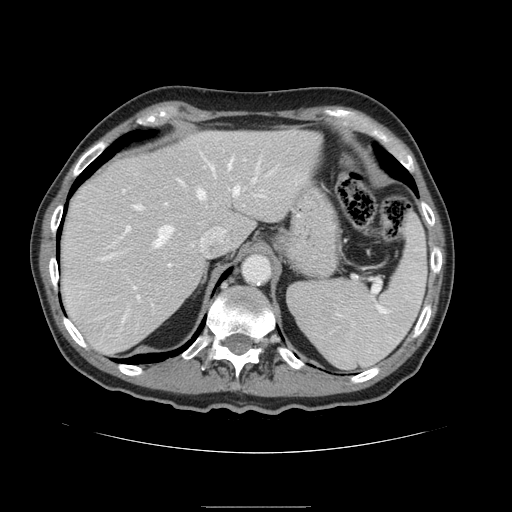
Contrast-enhanced abdominal CT, one axial slice. Position 115 of 168 along the scan axis. 120 kVp. Soft-tissue window (W 400 / L 40 HU). 2.5 mm slice thickness. 512 × 512 image matrix, field of view 386 × 386 mm. Male patient, age 74 years. Case-level facts recorded for this patient, not image findings: diagnosis: colorectal cancer liver metastases, imaged before liver resection; multiple liver metastases: no; largest metastasis: 14.5 cm; disease in both lobes: yes.
Annotated regions visible in this slice (outlined manually by an expert reader):
- hepatic veins: bounding box (x1, y1, x2, y2) in pixels: (106, 161, 273, 258)
- liver: (61, 130, 322, 355)
- planned liver remnant (the part of the liver to remain after resection): (61, 129, 322, 355)
- portal vein (with intrahepatic branches): (121, 195, 264, 299)